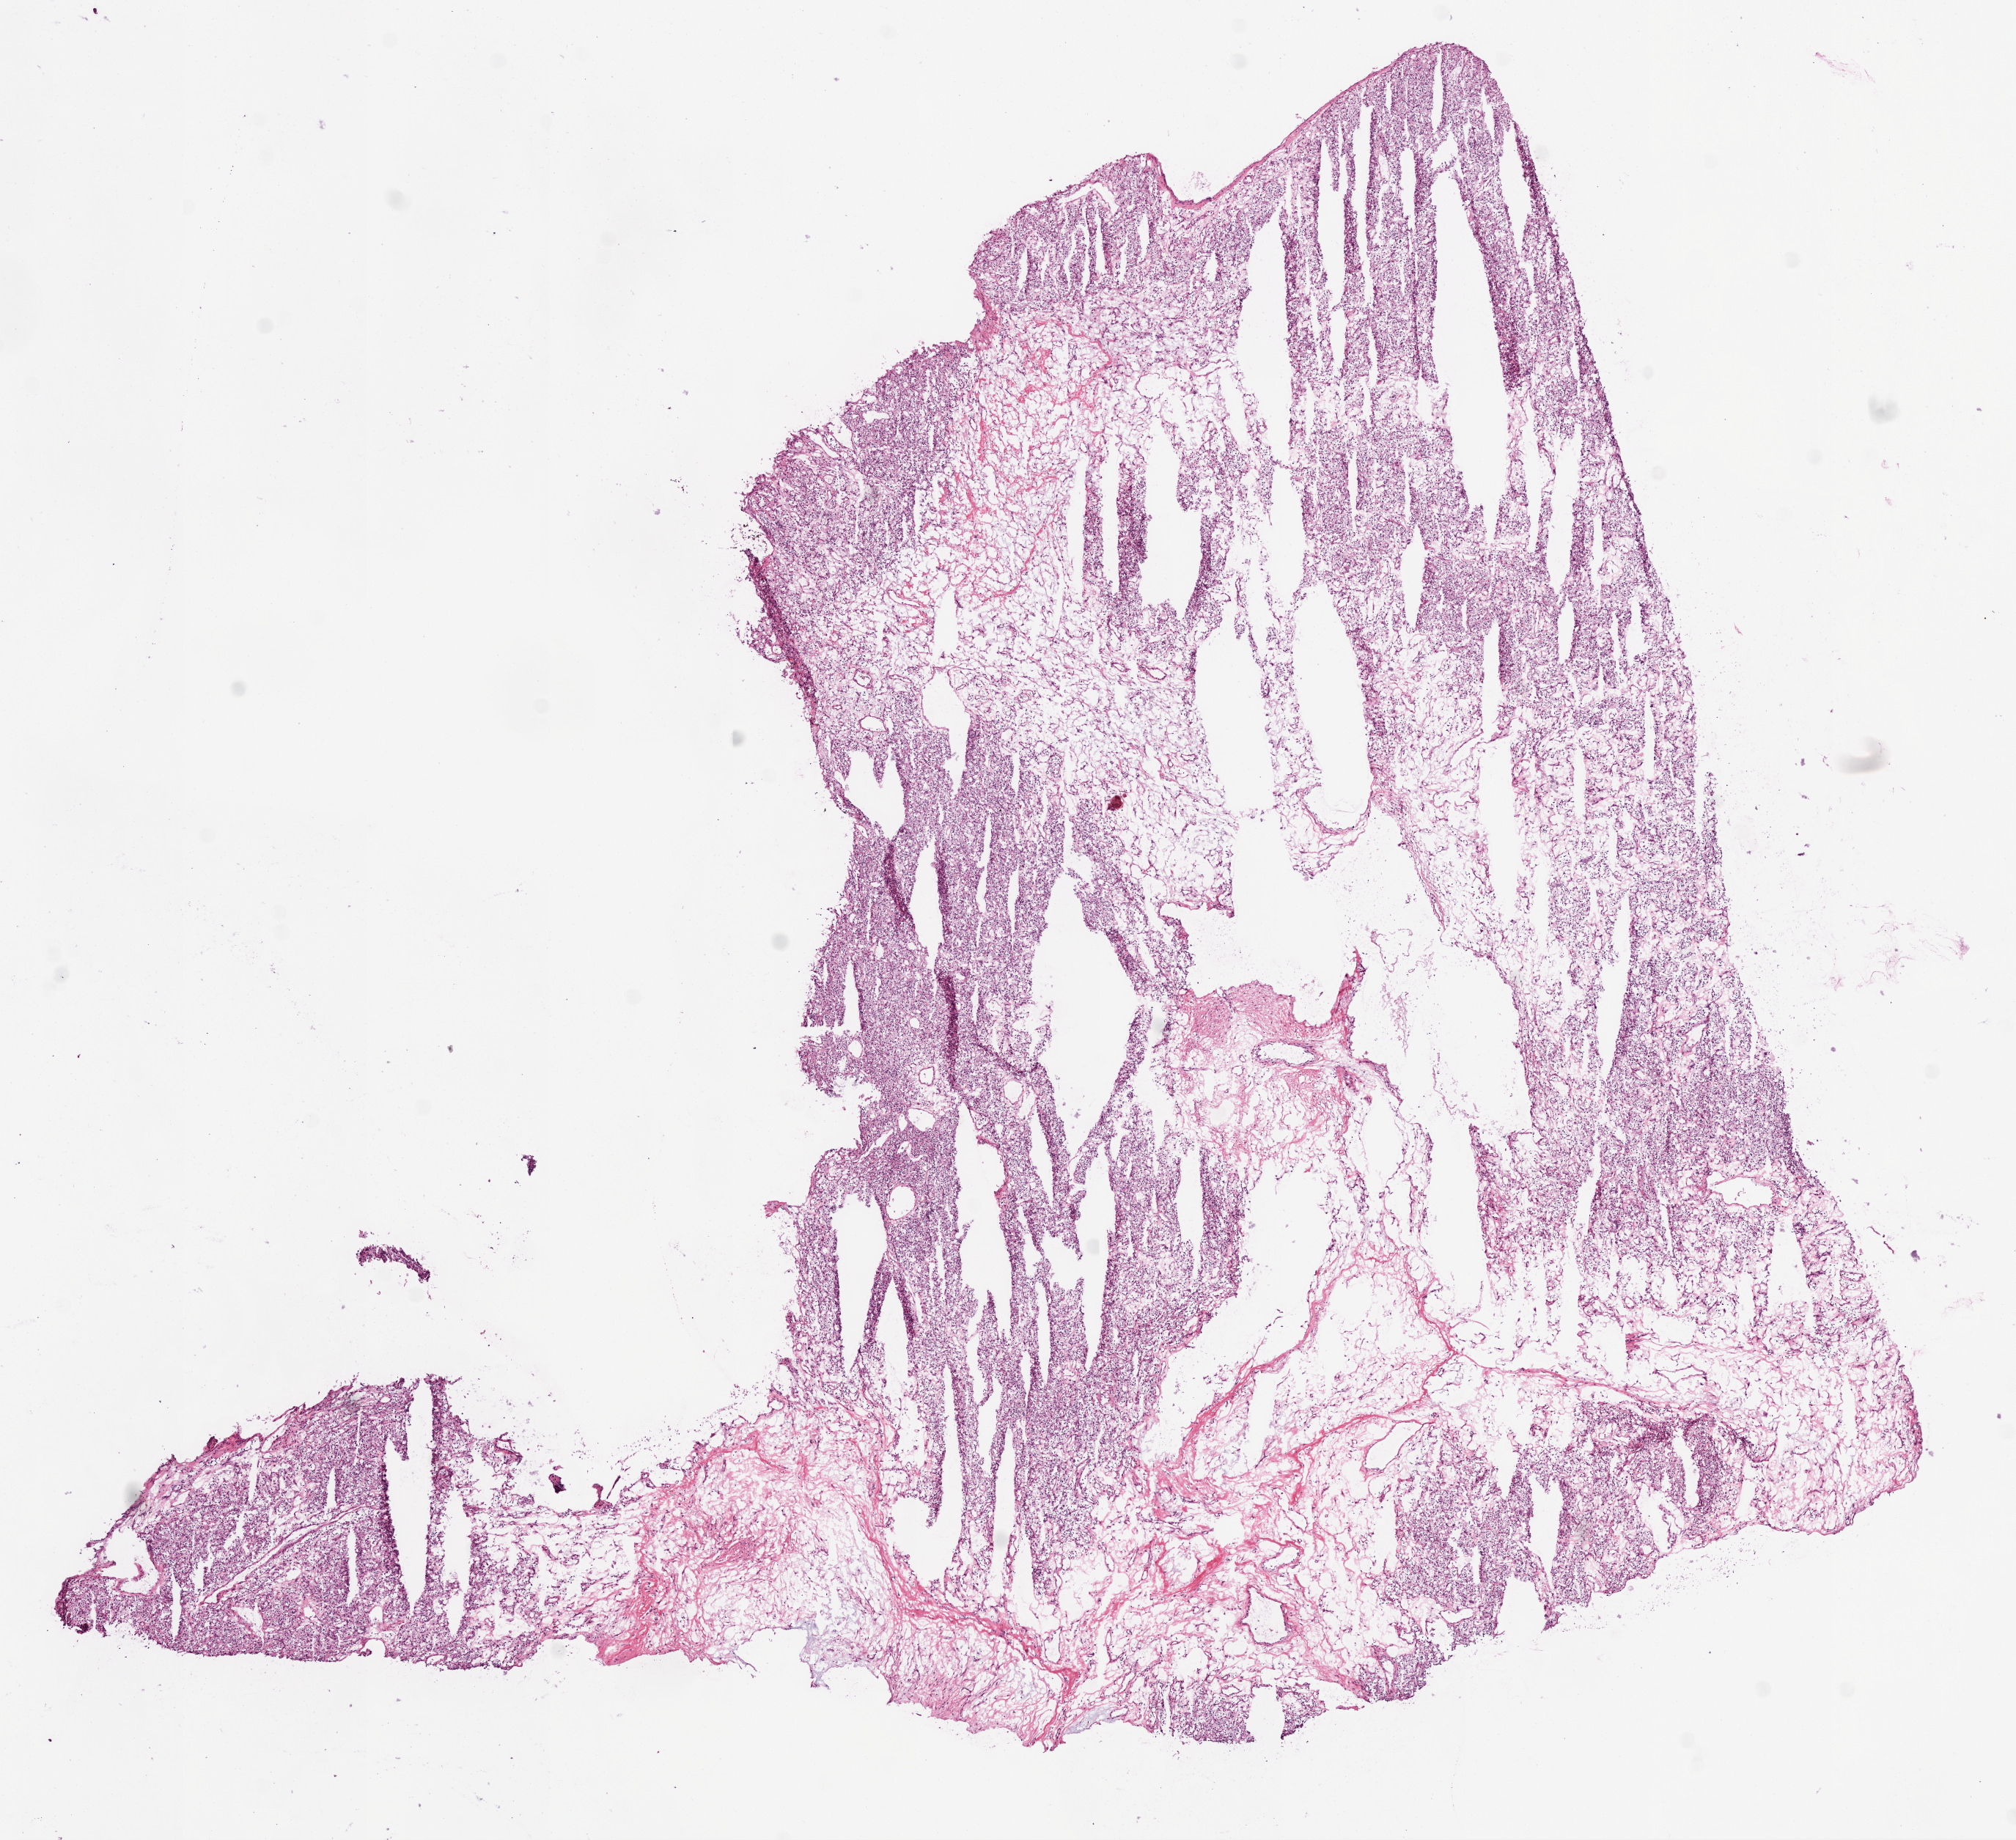
Digitized Hematoxylin and eosin (H&E) stained tissue section (whole slide), a low-resolution overview of the entire scanned area, about 11.0 x 10.1 mm, frozen section from the bottom of the tissue portion, sample: primary tumour, kidney. Male patient; age at initial diagnosis 70 years. Histologic grade: G2 (moderately differentiated). Composition of this section per pathologist review: tumour cells 55%, tumour nuclei 80%, normal cells 0%, stromal cells 45%, necrosis 0%.
AJCC pathologic stage: I. Pathologic diagnosis: Clear cell adenocarcinoma, NOS.